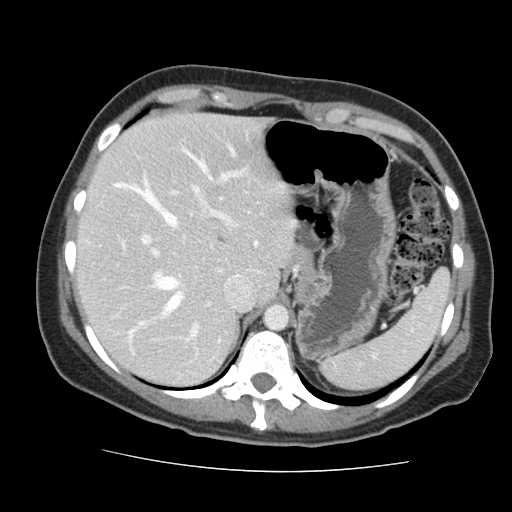
Contrast-enhanced abdominal CT, one axial slice. Slice 109 of 144 in the series (ordered by position). Intravenous contrast given. Soft-tissue window (W 400 / L 40 HU). 512 × 512 image matrix, field of view 333 × 333 mm. Female patient, age 46 years. Case-level facts recorded for this patient, not image findings: diagnosis: colorectal cancer liver metastases, imaged before liver resection; multiple liver metastases: no; largest metastasis: 2.8 cm; disease in both lobes: no.
Annotated regions visible in this slice (outlined manually by an expert reader):
- hepatic veins: box from (x=113, y=177) to (x=183, y=316) px
- liver: (x=79, y=114)–(x=291, y=385)
- planned liver remnant (the part of the liver to remain after resection): (x=79, y=114)–(x=291, y=385)
- portal vein (with intrahepatic branches): (x=128, y=172)–(x=241, y=340)